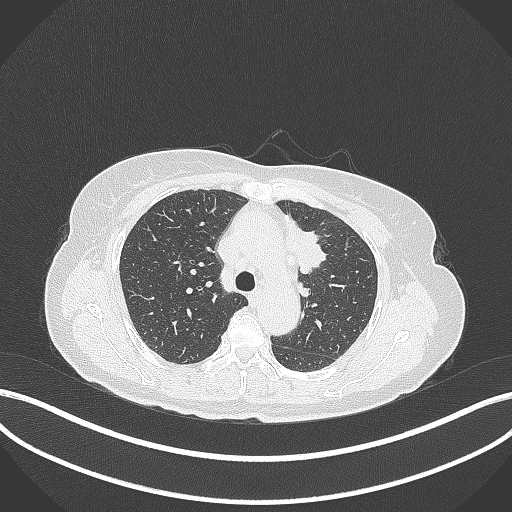
Chest CT, one axial slice; slice 237 of 369 in the series (ordered by position); 120 kVp; lung window (W 1500 / L -600 HU); 1 mm slice thickness; 512 × 512 image matrix, field of view 400 × 400 mm. Patient: female, 65 years. From the clinical record (not read from this slice): clinical TNM (as recorded): T2a N0 M0.
Structures marked on this image (bounding box drawn by a radiologist):
- lung tumour (recorded histology: adenocarcinoma): bounding box [x1, y1, x2, y2] px = [281, 219, 328, 275]